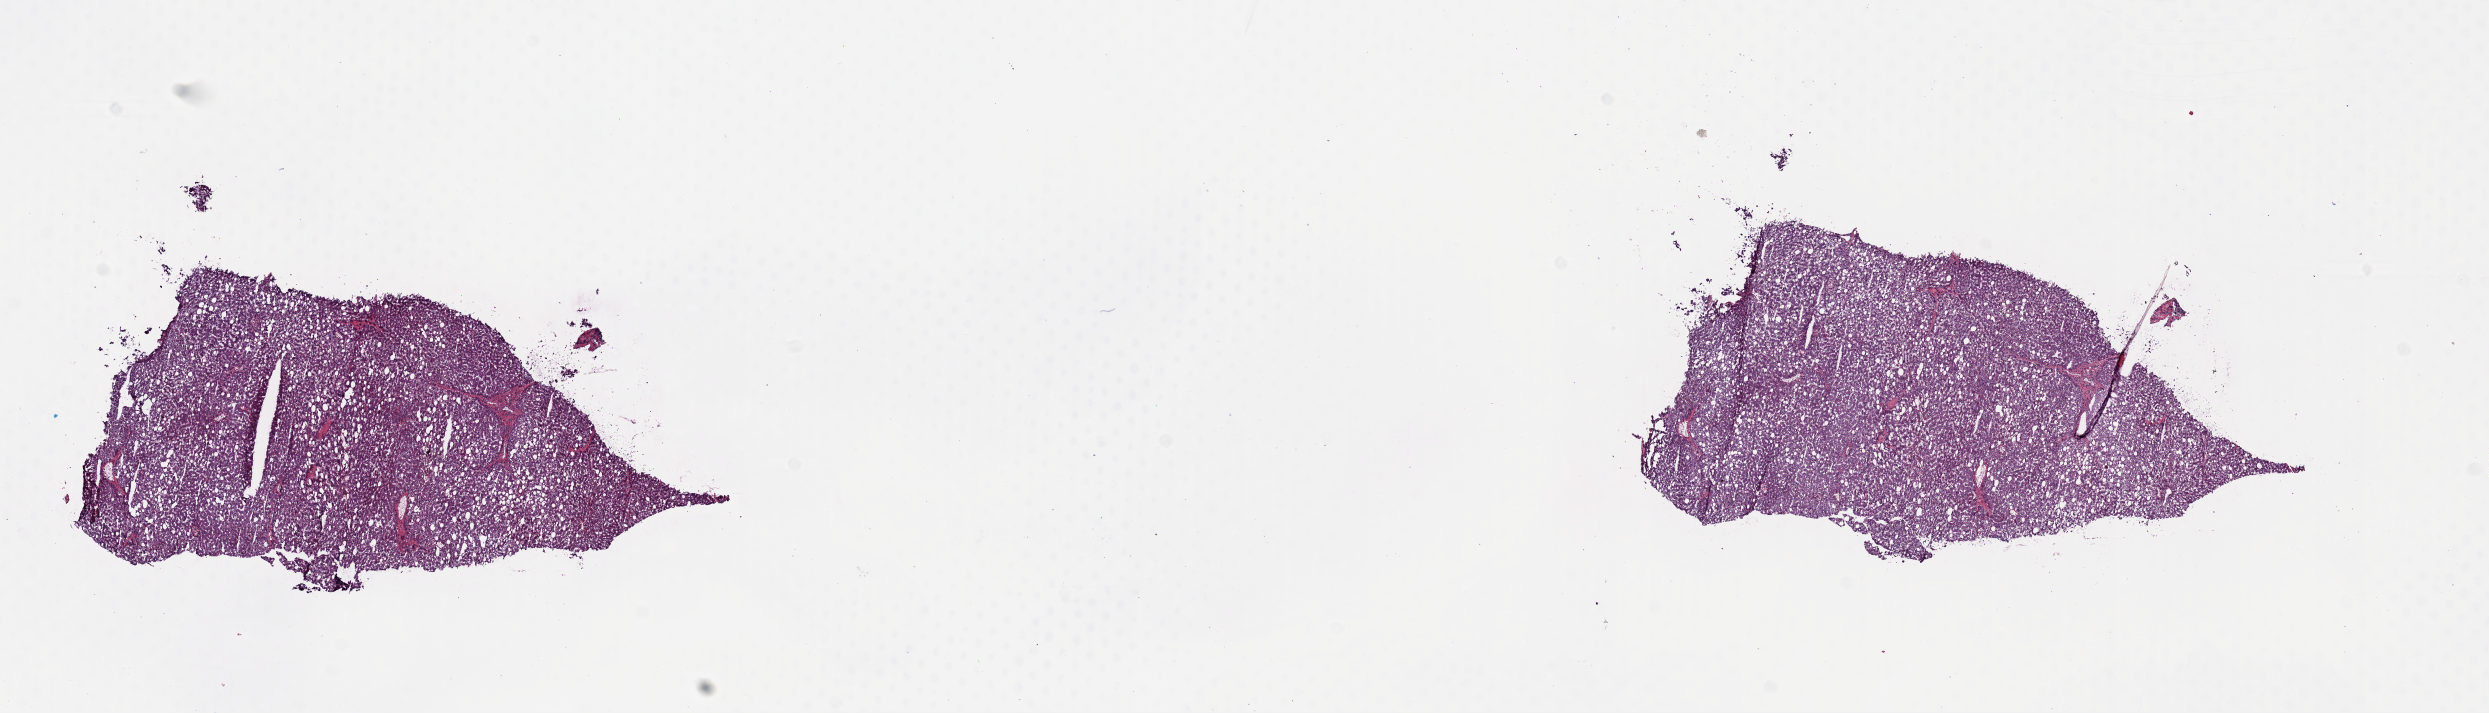
Whole-slide histology image, H&E — low-resolution overview of the scanned area, about 19.6 x 5.6 mm (slide scanned at 20x). Frozen section from the top of the tissue portion. Liver, solid tissue normal (non-tumour tissue) sample. Patient: male, age at initial diagnosis 60 years. Composition of this section per pathologist review: tumour cells 0%, tumour nuclei 0%, normal cells 100%, stromal cells 0%, necrosis 0%. Infiltration values recorded for this section: lymphocyte infiltration 2%, monocyte infiltration 0%, neutrophil infiltration 0%.
* this section: solid tissue normal (non-tumour) sample from the same patient
* patient diagnosis: Hepatocellular carcinoma, NOS